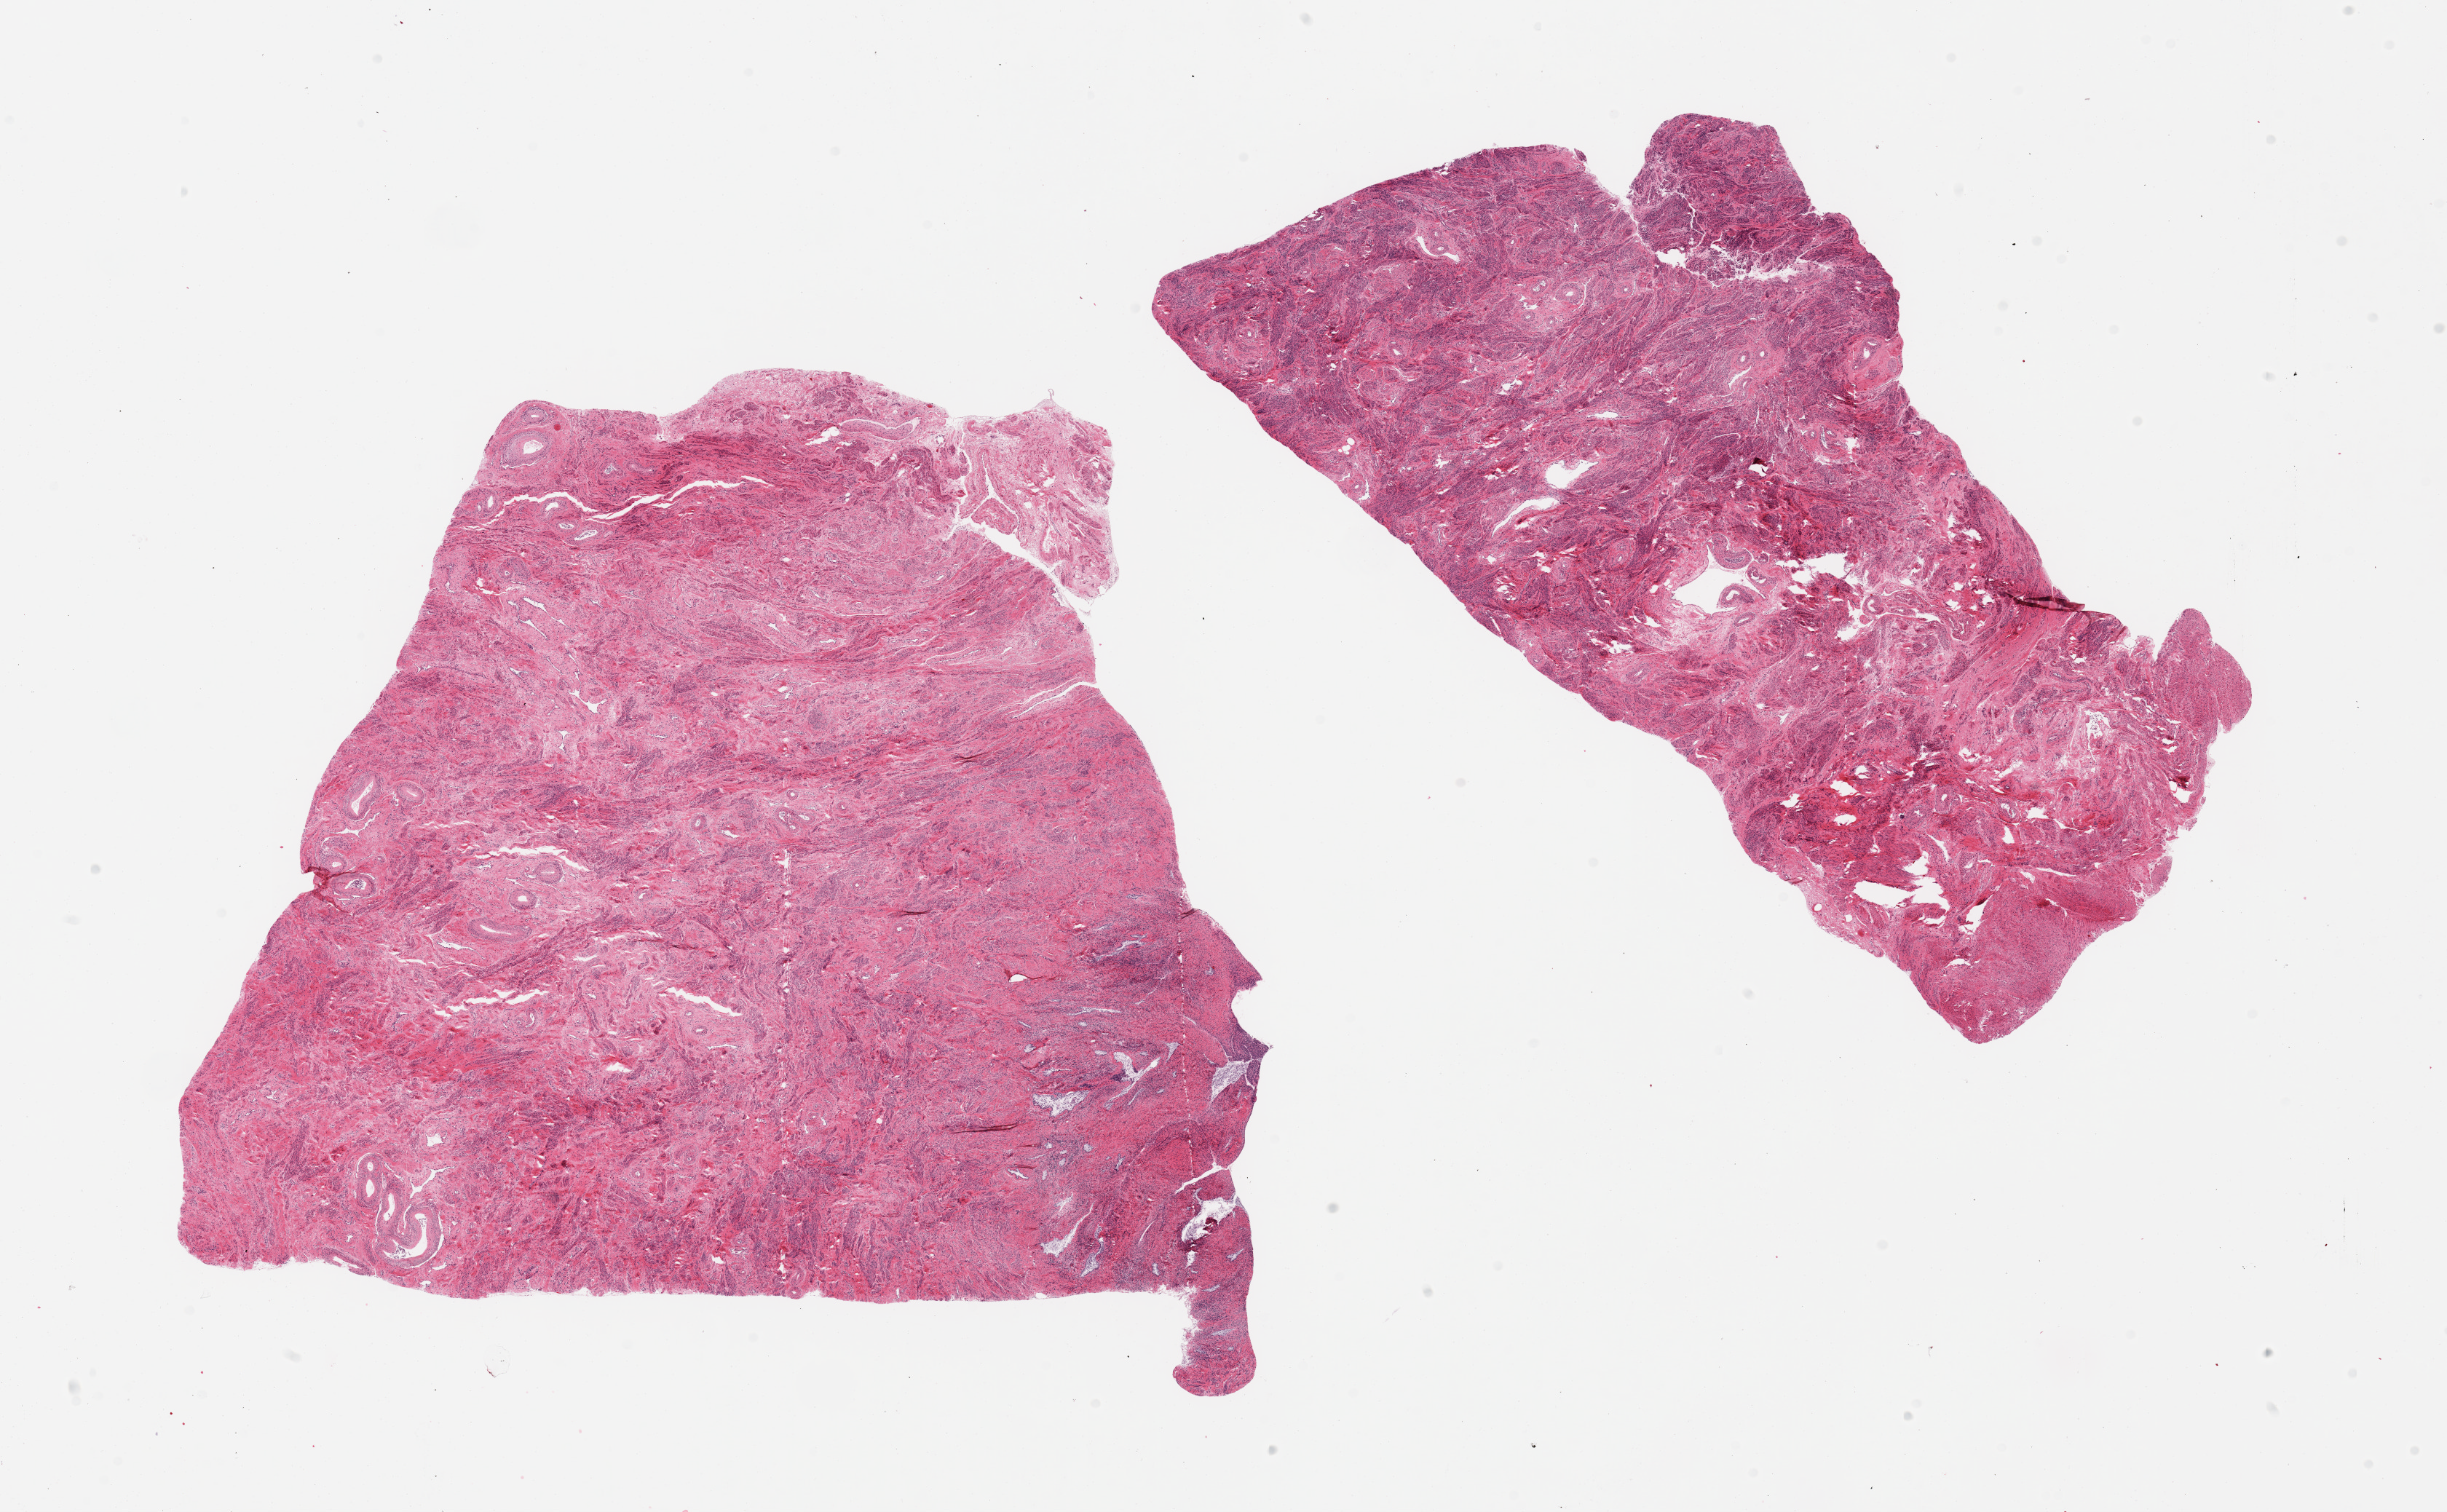
Whole-slide image, H&E stain, brightfield, shown as a low-resolution overview of the whole scanned area (about 26.6 x 16.4 mm, slide scanned at 20x). PAXgene-fixed paraffin-embedded (PFPE) section. Sampled site (target tissue): uterus. Tissue donor sample. Donor sex: female.
Pathologist's review note for this sample: 2 pieces: mostly myometrium; endometrium.